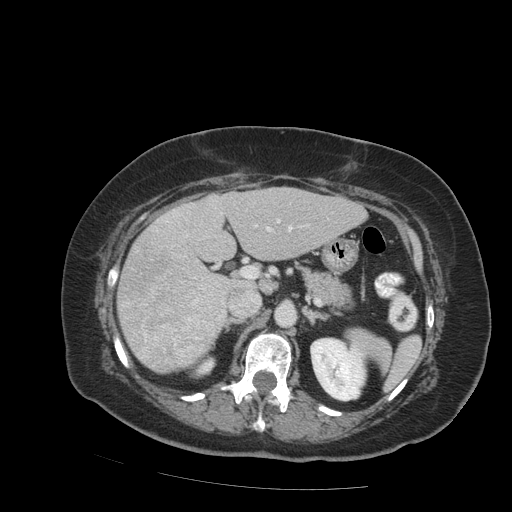
Contrast-enhanced abdominal CT (liver protocol), one axial slice; position 45 of 99 along the scan axis; reconstruction kernel STANDARD; soft-tissue window (W 400 / L 40 HU); 2.5 mm slice thickness; 512 × 512 image matrix, field of view 400 × 400 mm. Case-level facts recorded for this patient, not image findings: diagnosis: hepatocellular carcinoma (patient treated with transarterial chemoembolisation; whether this scan precedes or follows treatment is not stated here); TNM stage (as recorded): Stage-IVB; Child-Pugh class: A; tumour nodularity: uninodular.
Outlined on this slice (semi-automatic segmentation, software-assisted and operator-edited):
- liver parenchyma outside the tumour (the mass and vessels are separate outlines, so this box may not span the whole liver): bounding box [x1, y1, x2, y2] px = [116, 186, 366, 372]
- mass: [118, 241, 231, 372]
- liver vessels: [186, 219, 293, 237]